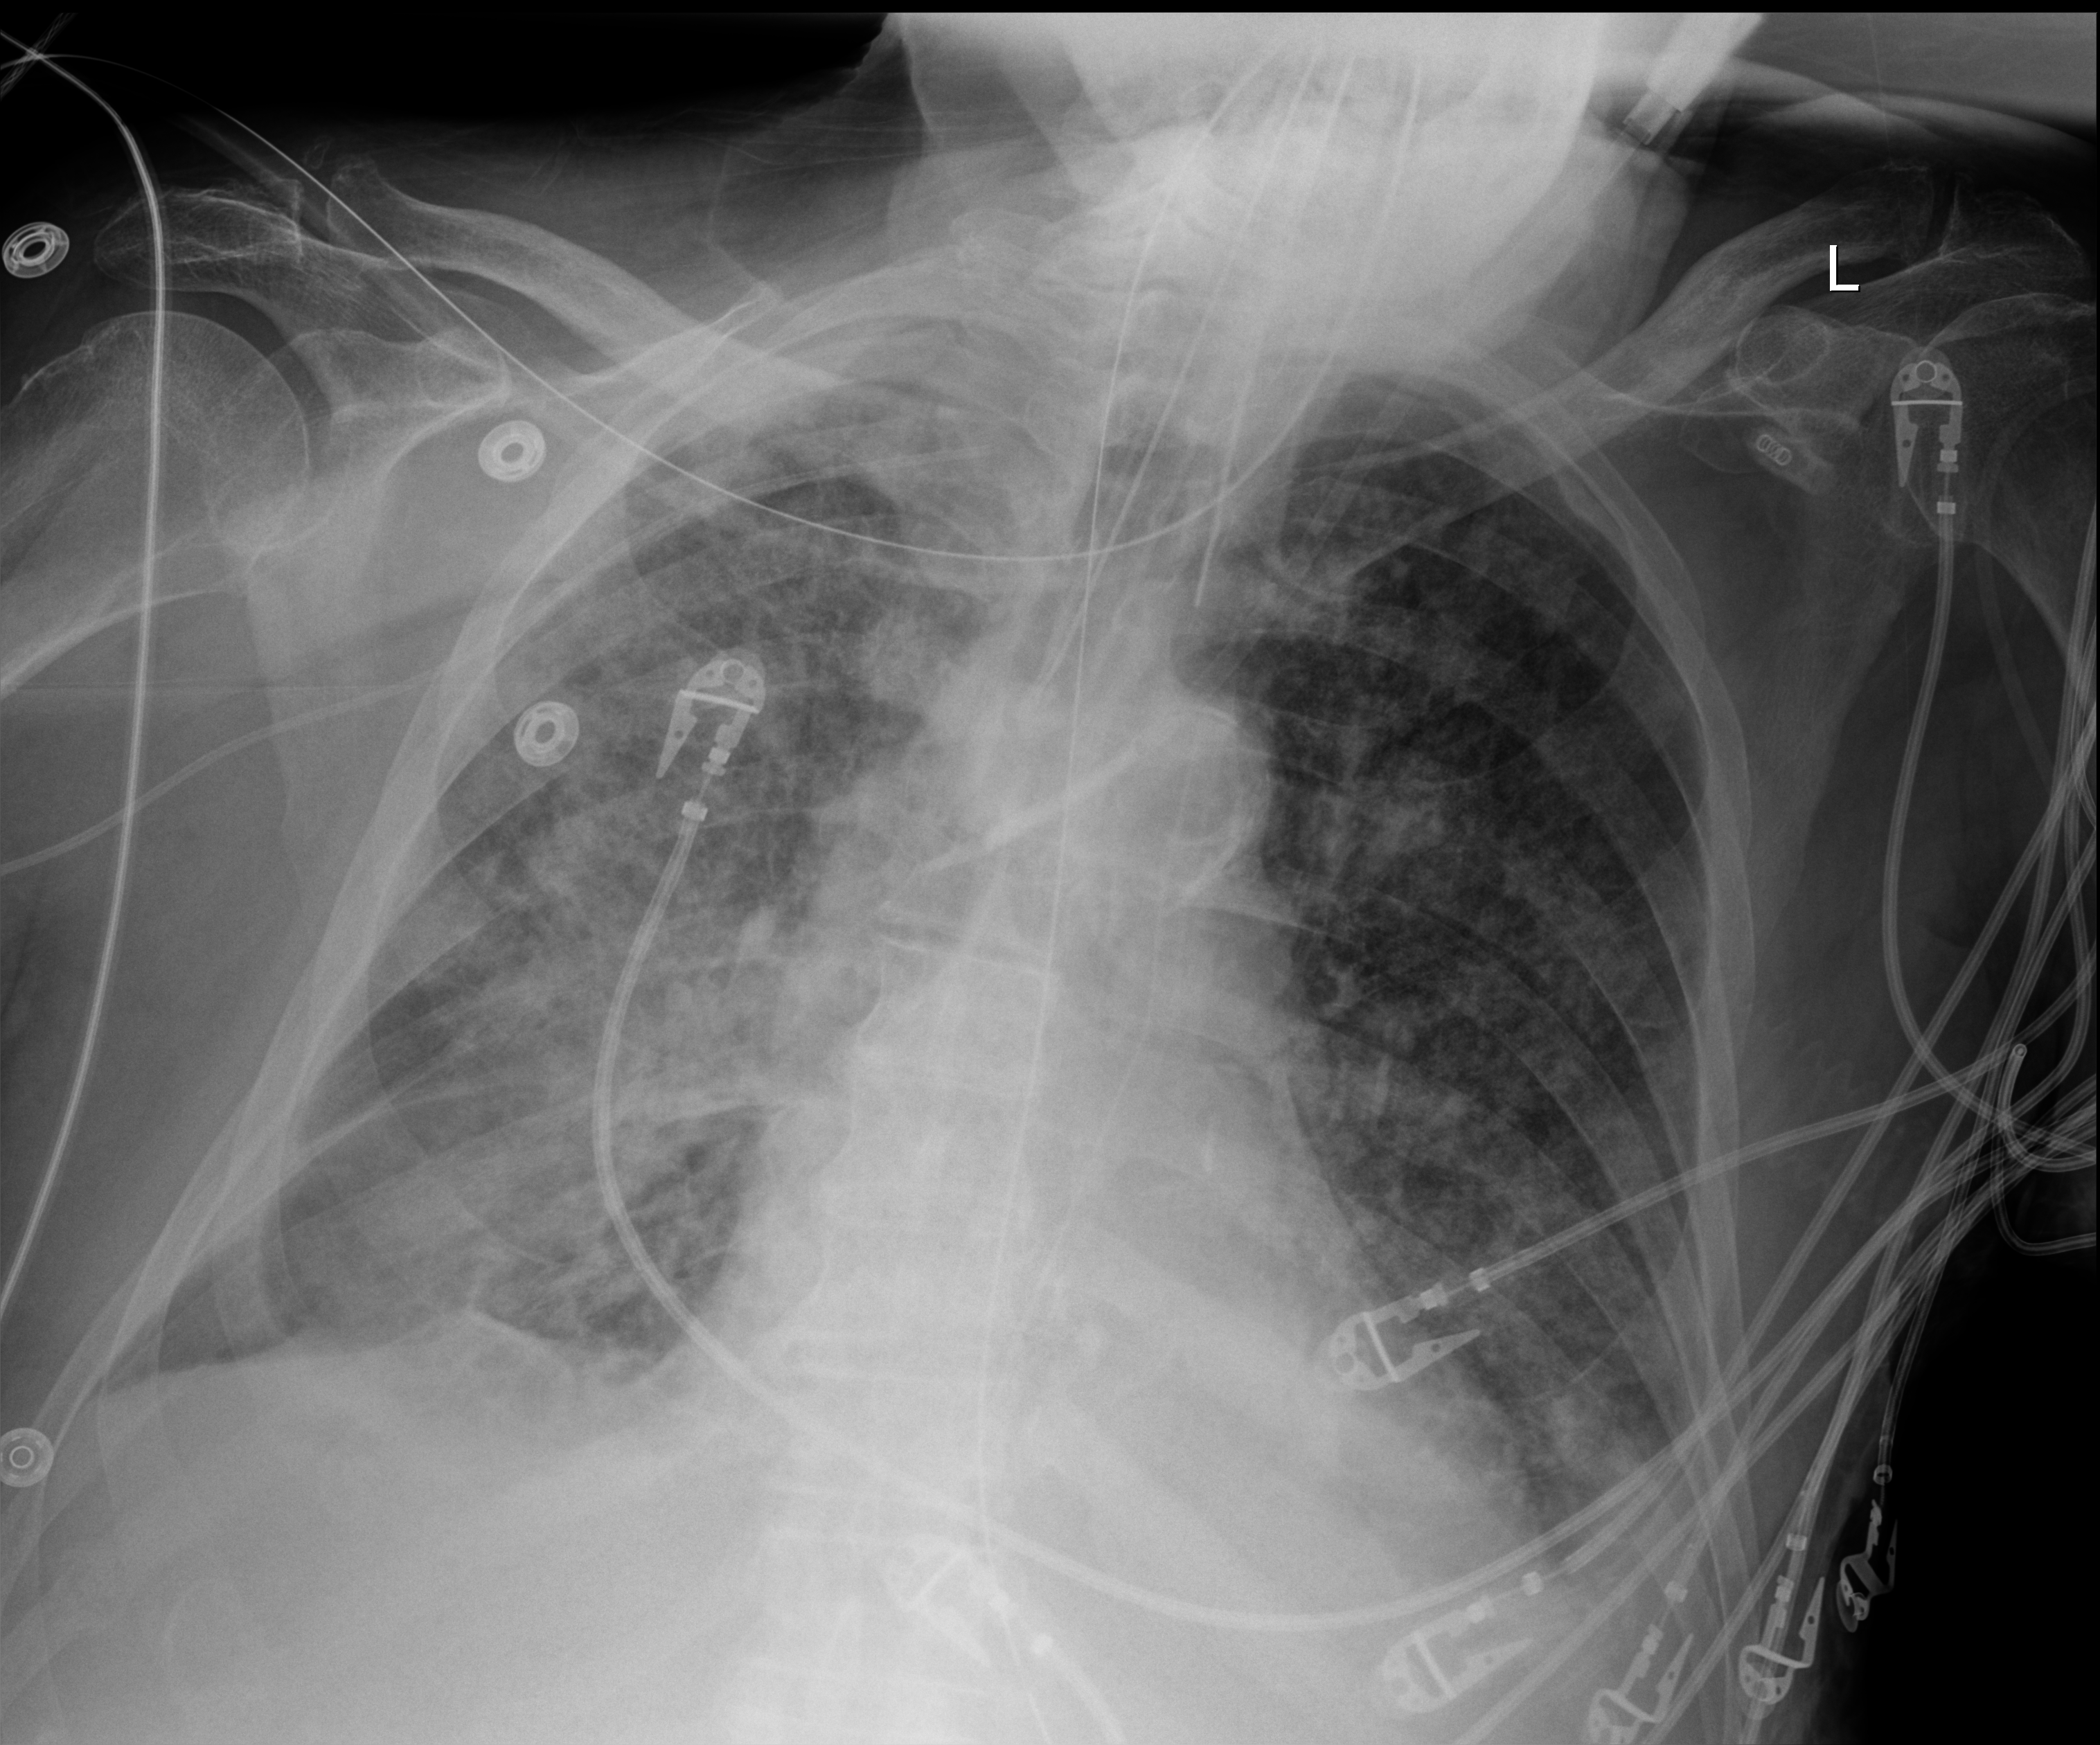
Portable chest radiograph, anteroposterior (AP) projection. Patient hospitalised with COVID-19; male, aged 75–90 years.
Hospital-stay facts (about this admission, not read from this image; timing relative to this image not recorded):
- admitted to intensive care during this hospital stay: yes